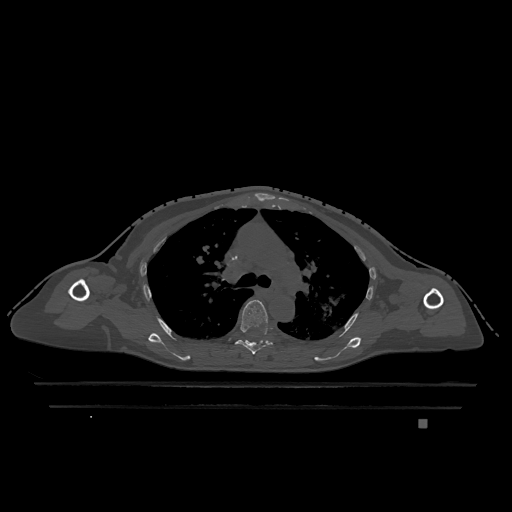
CT including the spine, one axial slice; slice 835 of 1317 in the series (ordered by position); bone window (W 1800 / L 400 HU); 0.5 mm slice thickness; 512 × 512 image matrix, field of view 500 × 500 mm. Patient: female, 74 years. Case-level facts recorded for this patient, not image findings: primary cancer: lung; vertebrae with lytic lesions (as recorded): T1, T4, T5, T6, L4, L5.
Annotated regions visible in this slice (semi-automatic segmentation, software-assisted and operator-edited):
- T5 vertebra: bounding box (x1, y1, x2, y2) in pixels: (235, 300, 273, 354)